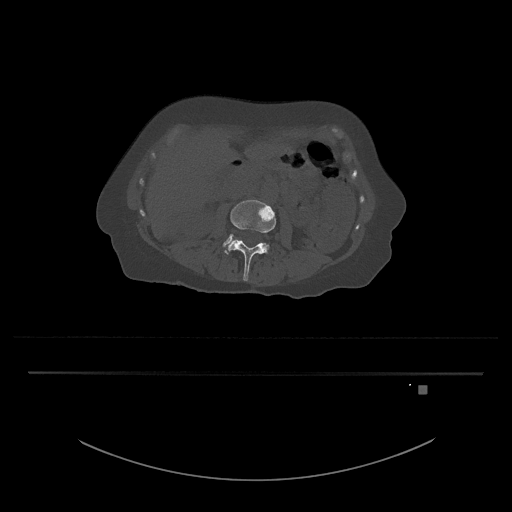
CT including the spine, one axial slice; slice 418 of 797 in the series (ordered by position); 120 kVp; bone window (W 1800 / L 400 HU); 0.5 mm slice thickness; 512 × 512 image matrix, field of view 500 × 500 mm. Patient: female, 57 years. From the clinical record (not read from this slice): primary cancer: cervical.
Structures marked on this image (semi-automatically segmented with operator editing):
- L3 vertebra: box from (x=224, y=200) to (x=276, y=281) px
- L4 vertebra: (x=223, y=234)–(x=232, y=247)